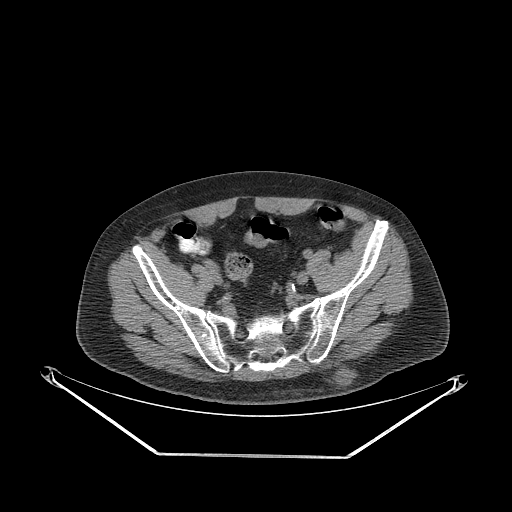
CT of an extremity soft-tissue mass (from a PET/CT study), one axial slice. Slice 72 of 267 in the series (ordered by position). 140 kVp. Soft-tissue window (W 400 / L 40 HU). 3.75 mm slice thickness. 512 × 512 image matrix, field of view 500 × 500 mm. Male patient. From the clinical record (not read from this slice): histological type: leiomyosarcoma; grade: intermediate; site of the primary tumour: left pelvis.
Structures marked on this image (expert contour drawn on MRI and transferred to this co-registered scan by the dataset authors):
- gross tumour volume (mass): bounding box (x1, y1, x2, y2) in pixels: (336, 372, 353, 385)